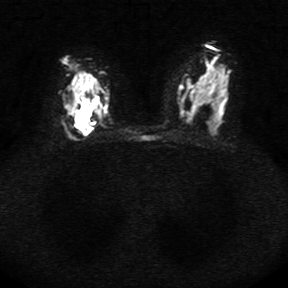
Breast MRI, one axial slice. Position 17 of 34 along the scan axis. Diffusion-weighted series; image 2 of 4 stored at this slice position (different b-values; order by instance number). 1.5 T. 288 × 288 image matrix, field of view 340 × 340 mm. Female patient.
Structures marked on this image (expert manual segmentation):
- tumour on diffusion-weighted imaging: box from (x=71, y=106) to (x=91, y=132) px